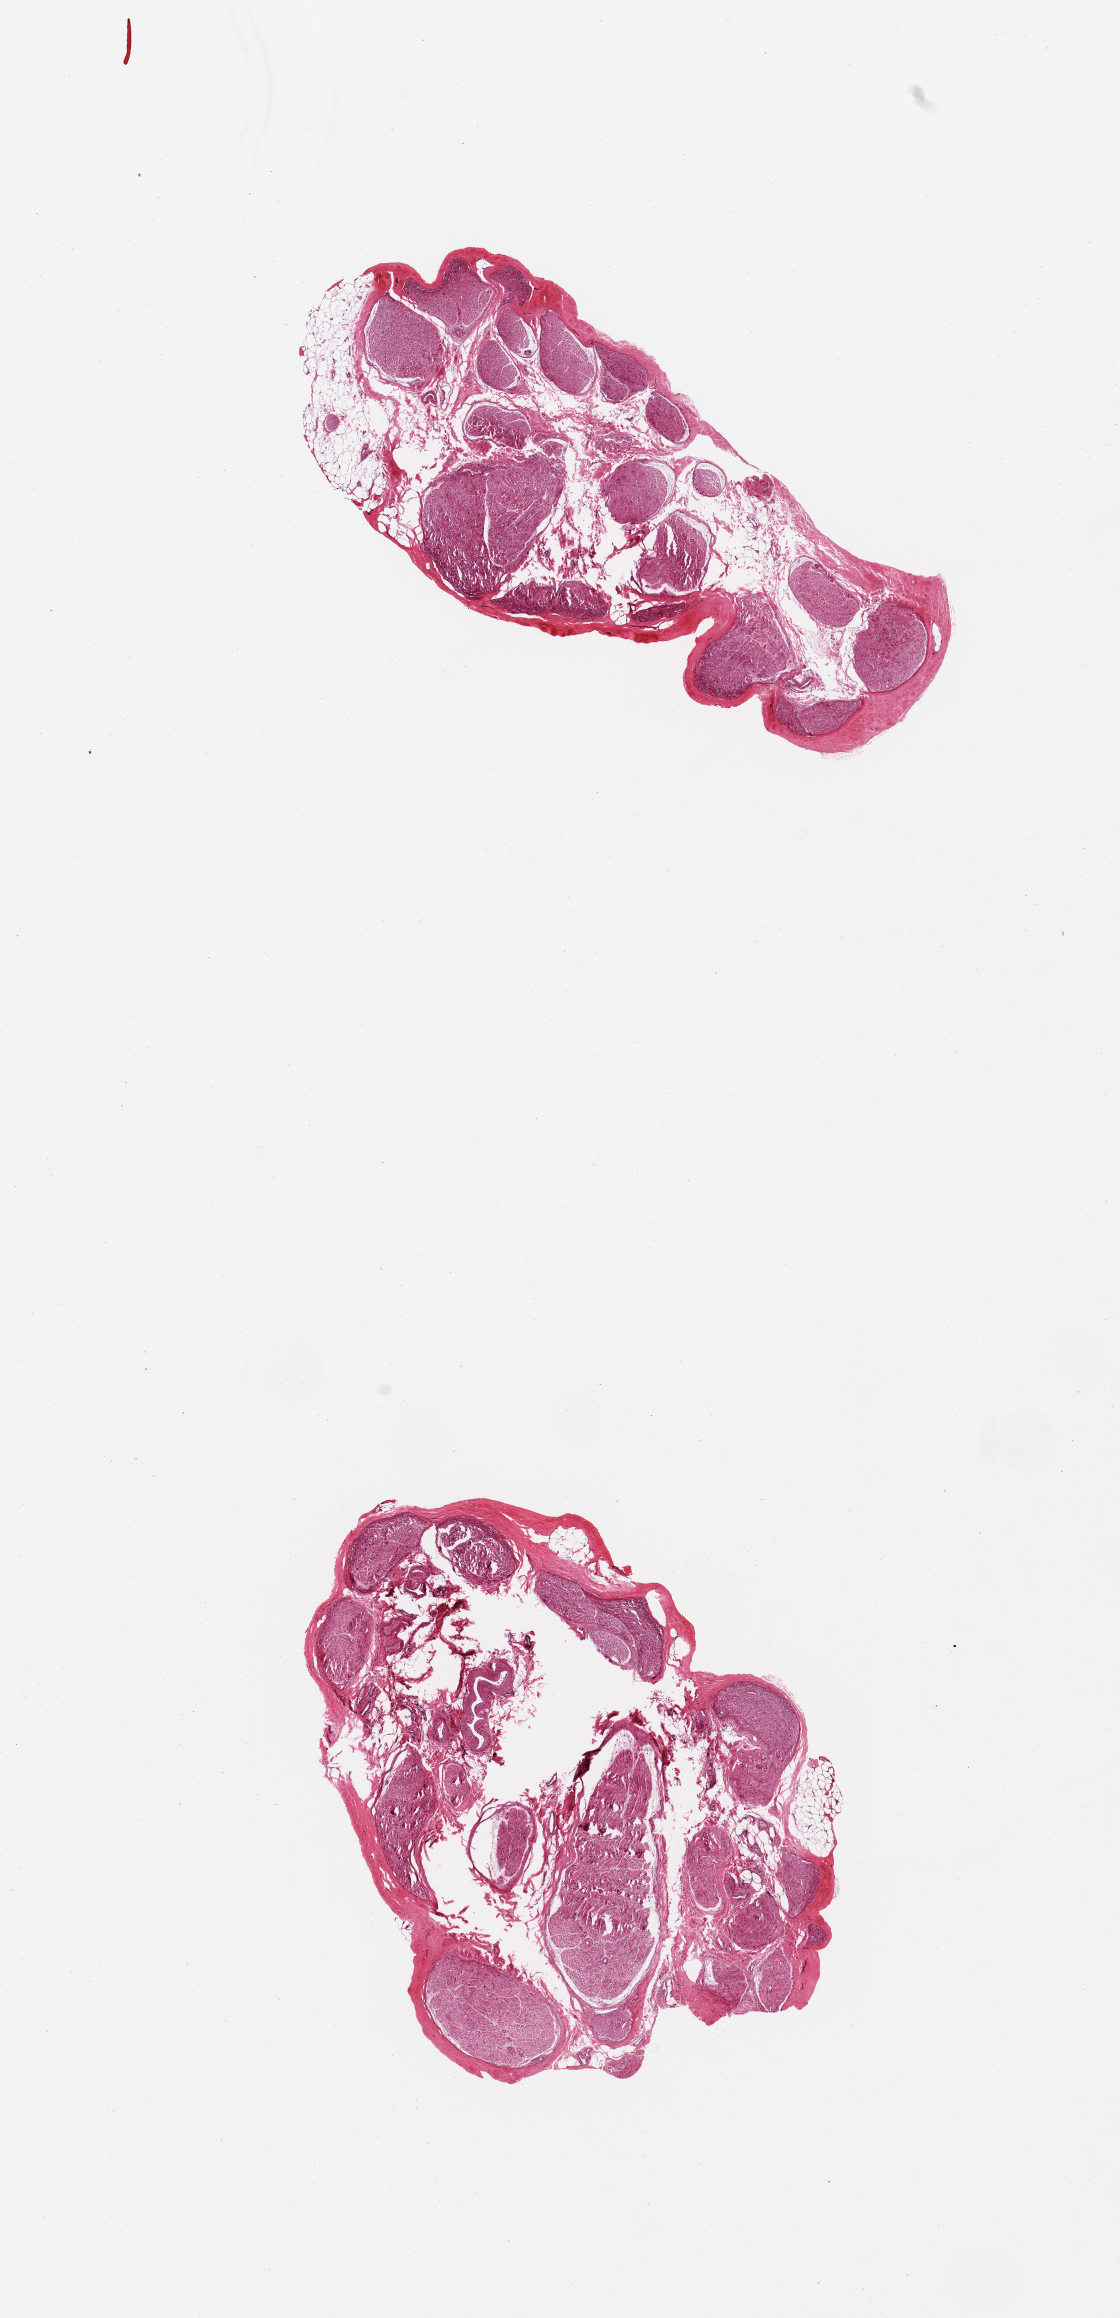
Hematoxylin and eosin (H&E) whole-slide image, brightfield, whole scanned area (about 8.9 x 18.3 mm, from a 20x scan) shown as a low-resolution overview; PAXgene-fixed paraffin-embedded (PFPE) section; section of tibial nerve (target tissue); tissue donor sample. Male donor.
Reviewer comment on this tissue sample: 2 pieces; 20% fat and stromal content.